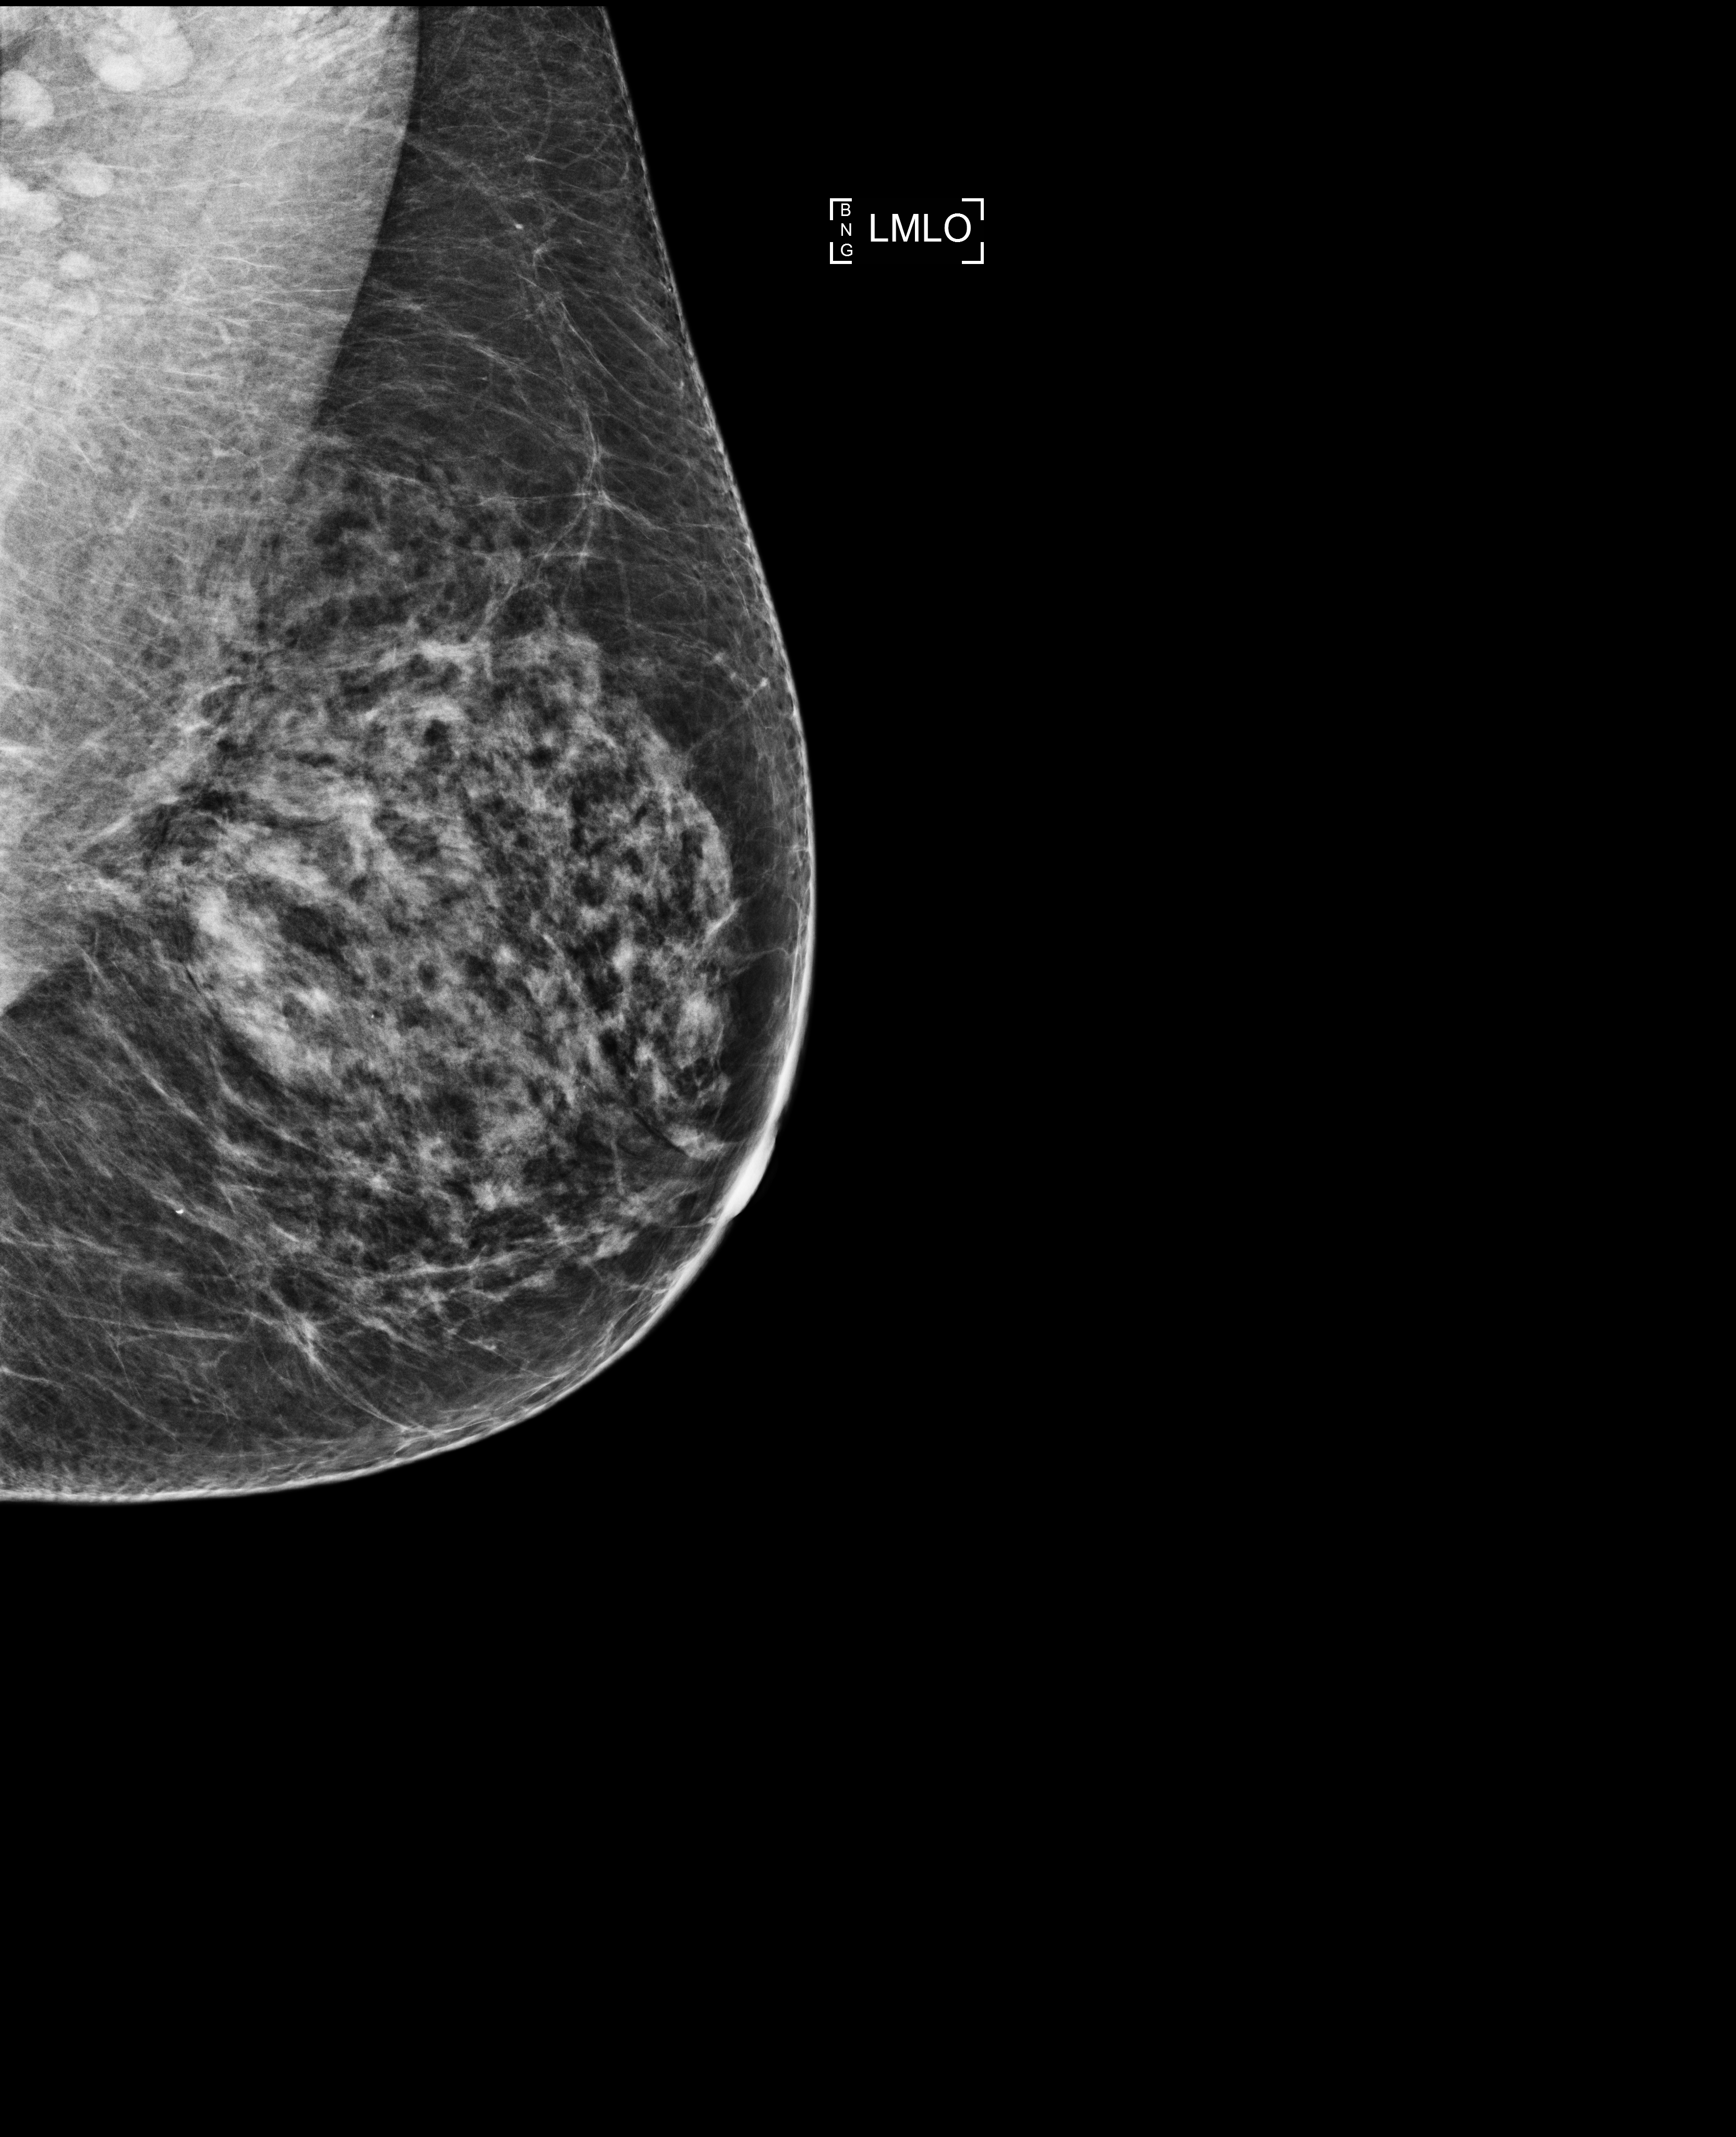
Annual screening mammography examination. Patient aged 62 years (female).
Image type: full-field digital mammogram. Breast: left. Projection: mediolateral oblique (MLO) view.